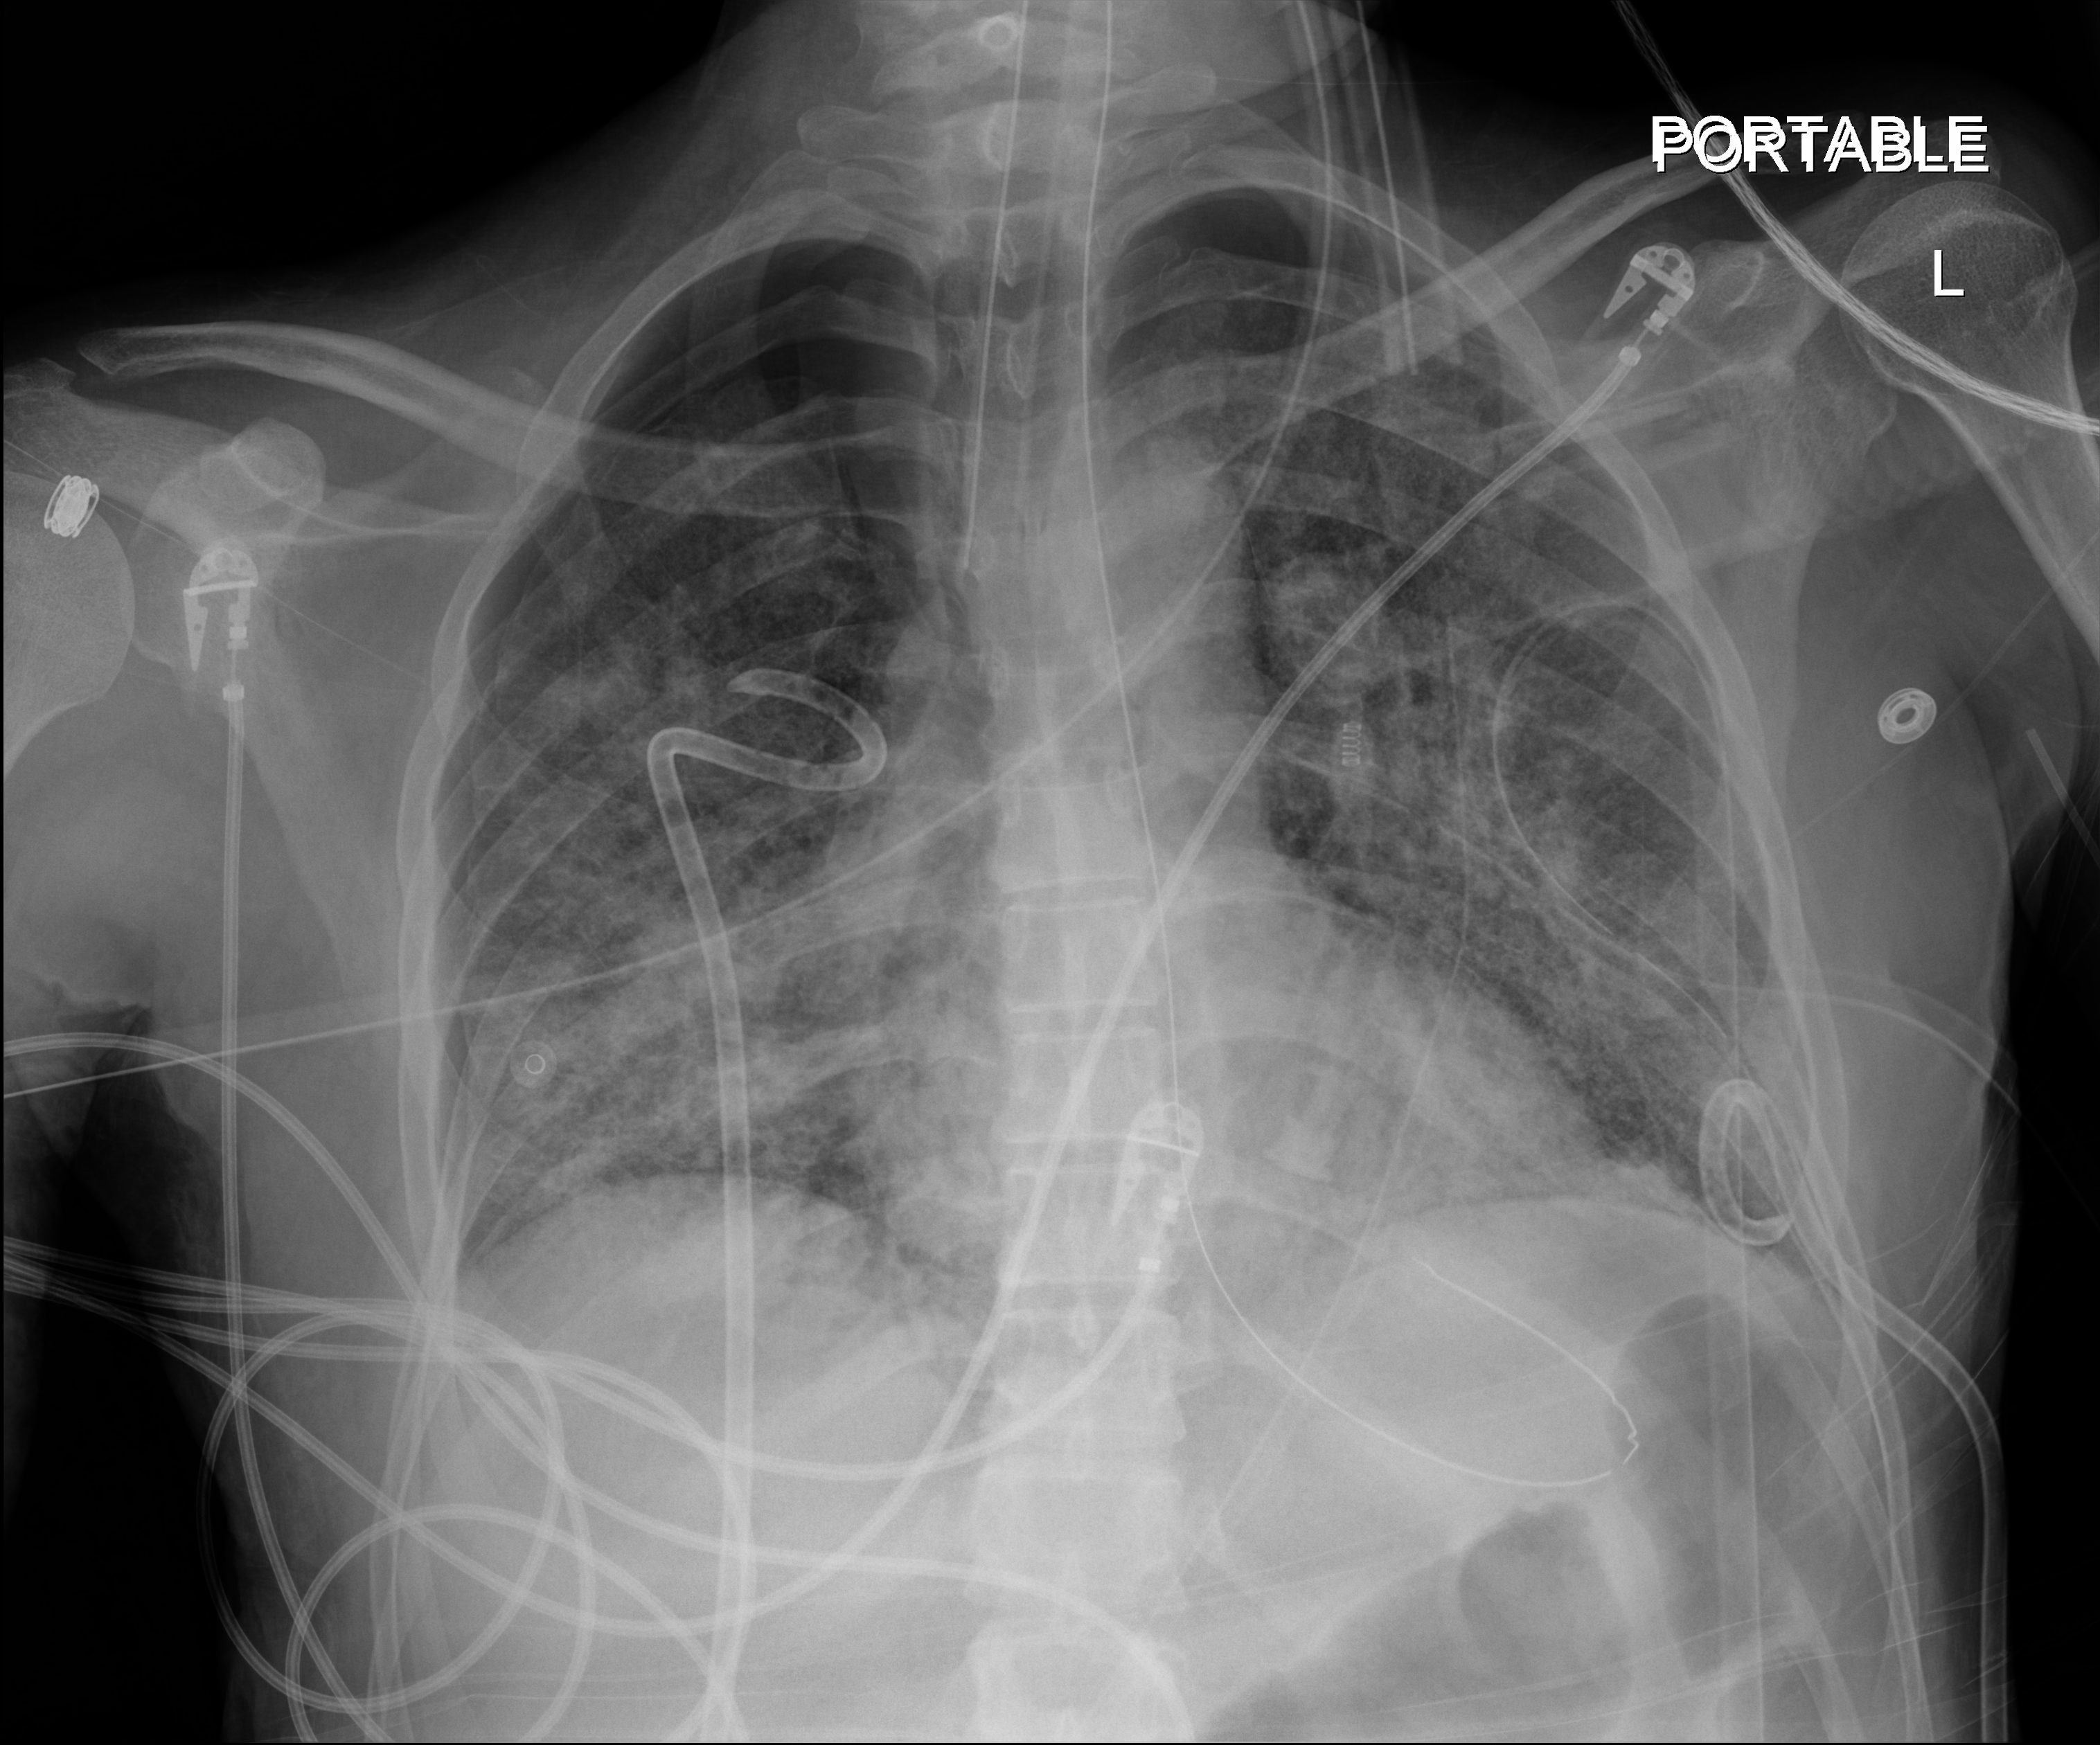
Portable chest radiograph, anteroposterior (AP) projection. Adult patient hospitalised with COVID-19, age 18–59 years.
From the hospital-stay record, not from the radiograph (when in the stay this image was taken is not recorded):
- admitted to intensive care during this hospital stay: yes
- mechanically ventilated during this hospital stay: yes